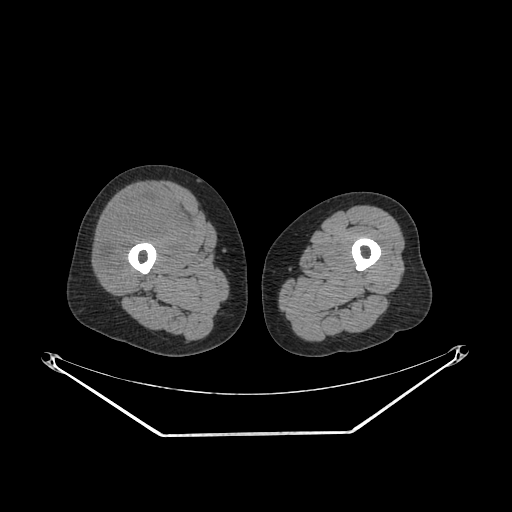
CT of an extremity soft-tissue mass (from a PET/CT study), one axial slice; slice 235 of 311 in the series (ordered by position); soft-tissue window (W 400 / L 40 HU); 3.75 mm slice thickness; 512 × 512 image matrix, field of view 500 × 500 mm. Female patient. From the clinical record (not read from this slice): histological type: pleiomorphic undifferentiated sarcoma; grade: high; site of the primary tumour: right quadricep.
Structures marked on this image (expert contour drawn on MRI and transferred to this co-registered scan by the dataset authors):
- tumour plus oedema (research contour): bounding box [x1, y1, x2, y2] px = [100, 196, 184, 282]
- tumour (research contour): [100, 196, 184, 282]